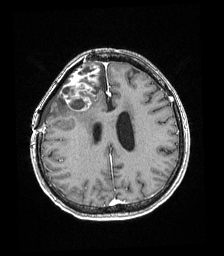
Brain MRI from a brain-tumour surgery series, one axial slice; position 72 of 192 along the scan axis; T1-weighted post-contrast; 1 mm slice thickness; 224 × 256 image matrix, field of view 219 × 250 mm. From the clinical record (not read from this slice): histopathology: Astrocytoma; WHO grade: 4; IDH mutation: yes.
Outlined on this slice (outlined manually by an expert reader):
- tumour: bounding box <60,62,100,112> (left, top, right, bottom; pixels)